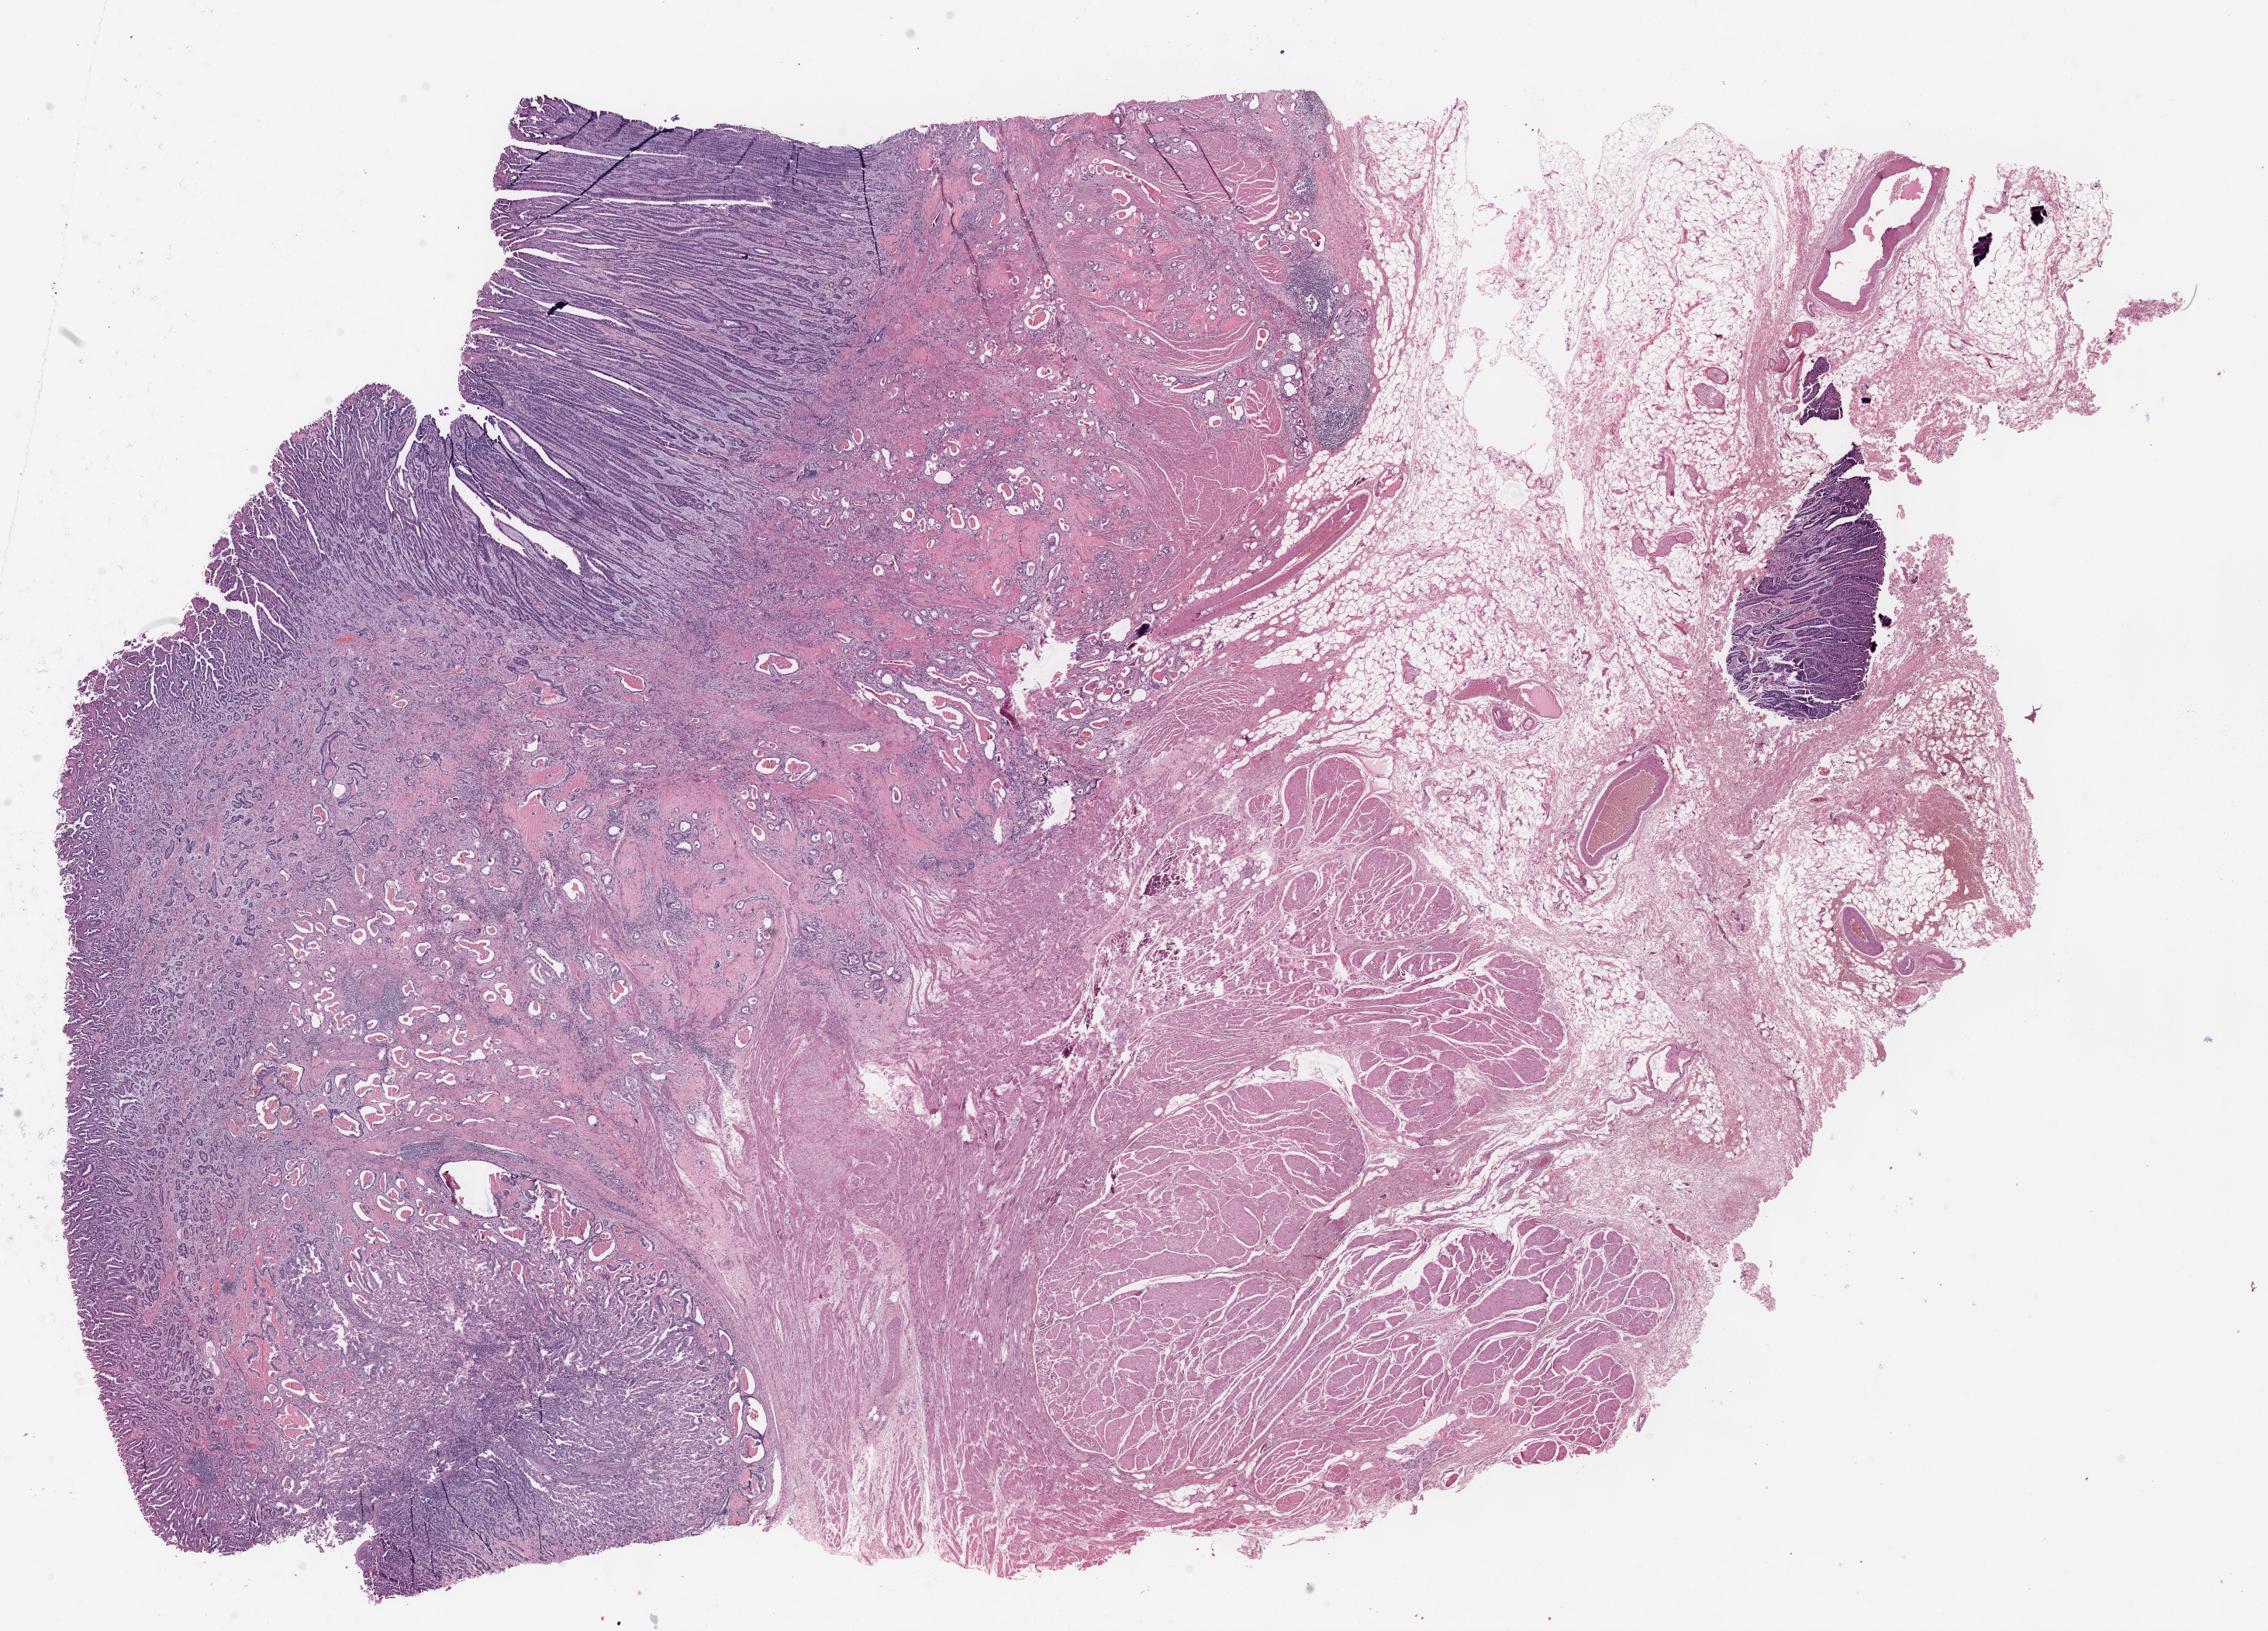
Whole-slide histology image, H&E-stained, whole scanned area (about 23.6 x 17.0 mm, from a 40x scan) shown as a low-resolution overview; formalin-fixed paraffin-embedded (FFPE) diagnostic section; stomach, primary tumour sample. Male, age 56 years at initial diagnosis. Histologic grade: G2 (moderately differentiated).
• diagnosis: Adenocarcinoma, intestinal type (cardia, NOS)
• TNM: T4 N3a M0
• lymph nodes positive (case pathology): 8 of 26 examined
• AJCC pathologic stage: IIIC (7th edition)